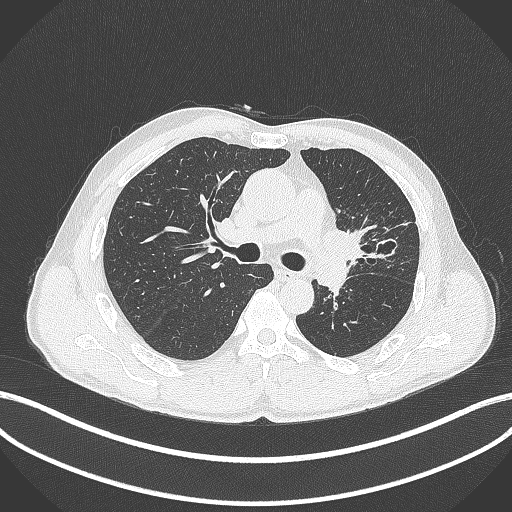
Chest CT, one axial slice; slice 261 of 429 in the series (ordered by position); reconstruction kernel B70f; 120 kVp; lung window (W 1500 / L -600 HU); 1 mm slice thickness; 512 × 512 image matrix, field of view 400 × 400 mm. Male patient, age 57 years. From the clinical record (not read from this slice): clinical TNM (as recorded): T2b N0 M0.
Structures marked on this image (rectangle marked by the reading radiologist):
- lung tumour (recorded histology: squamous cell carcinoma): bounding box [x1, y1, x2, y2] px = [323, 222, 379, 264]